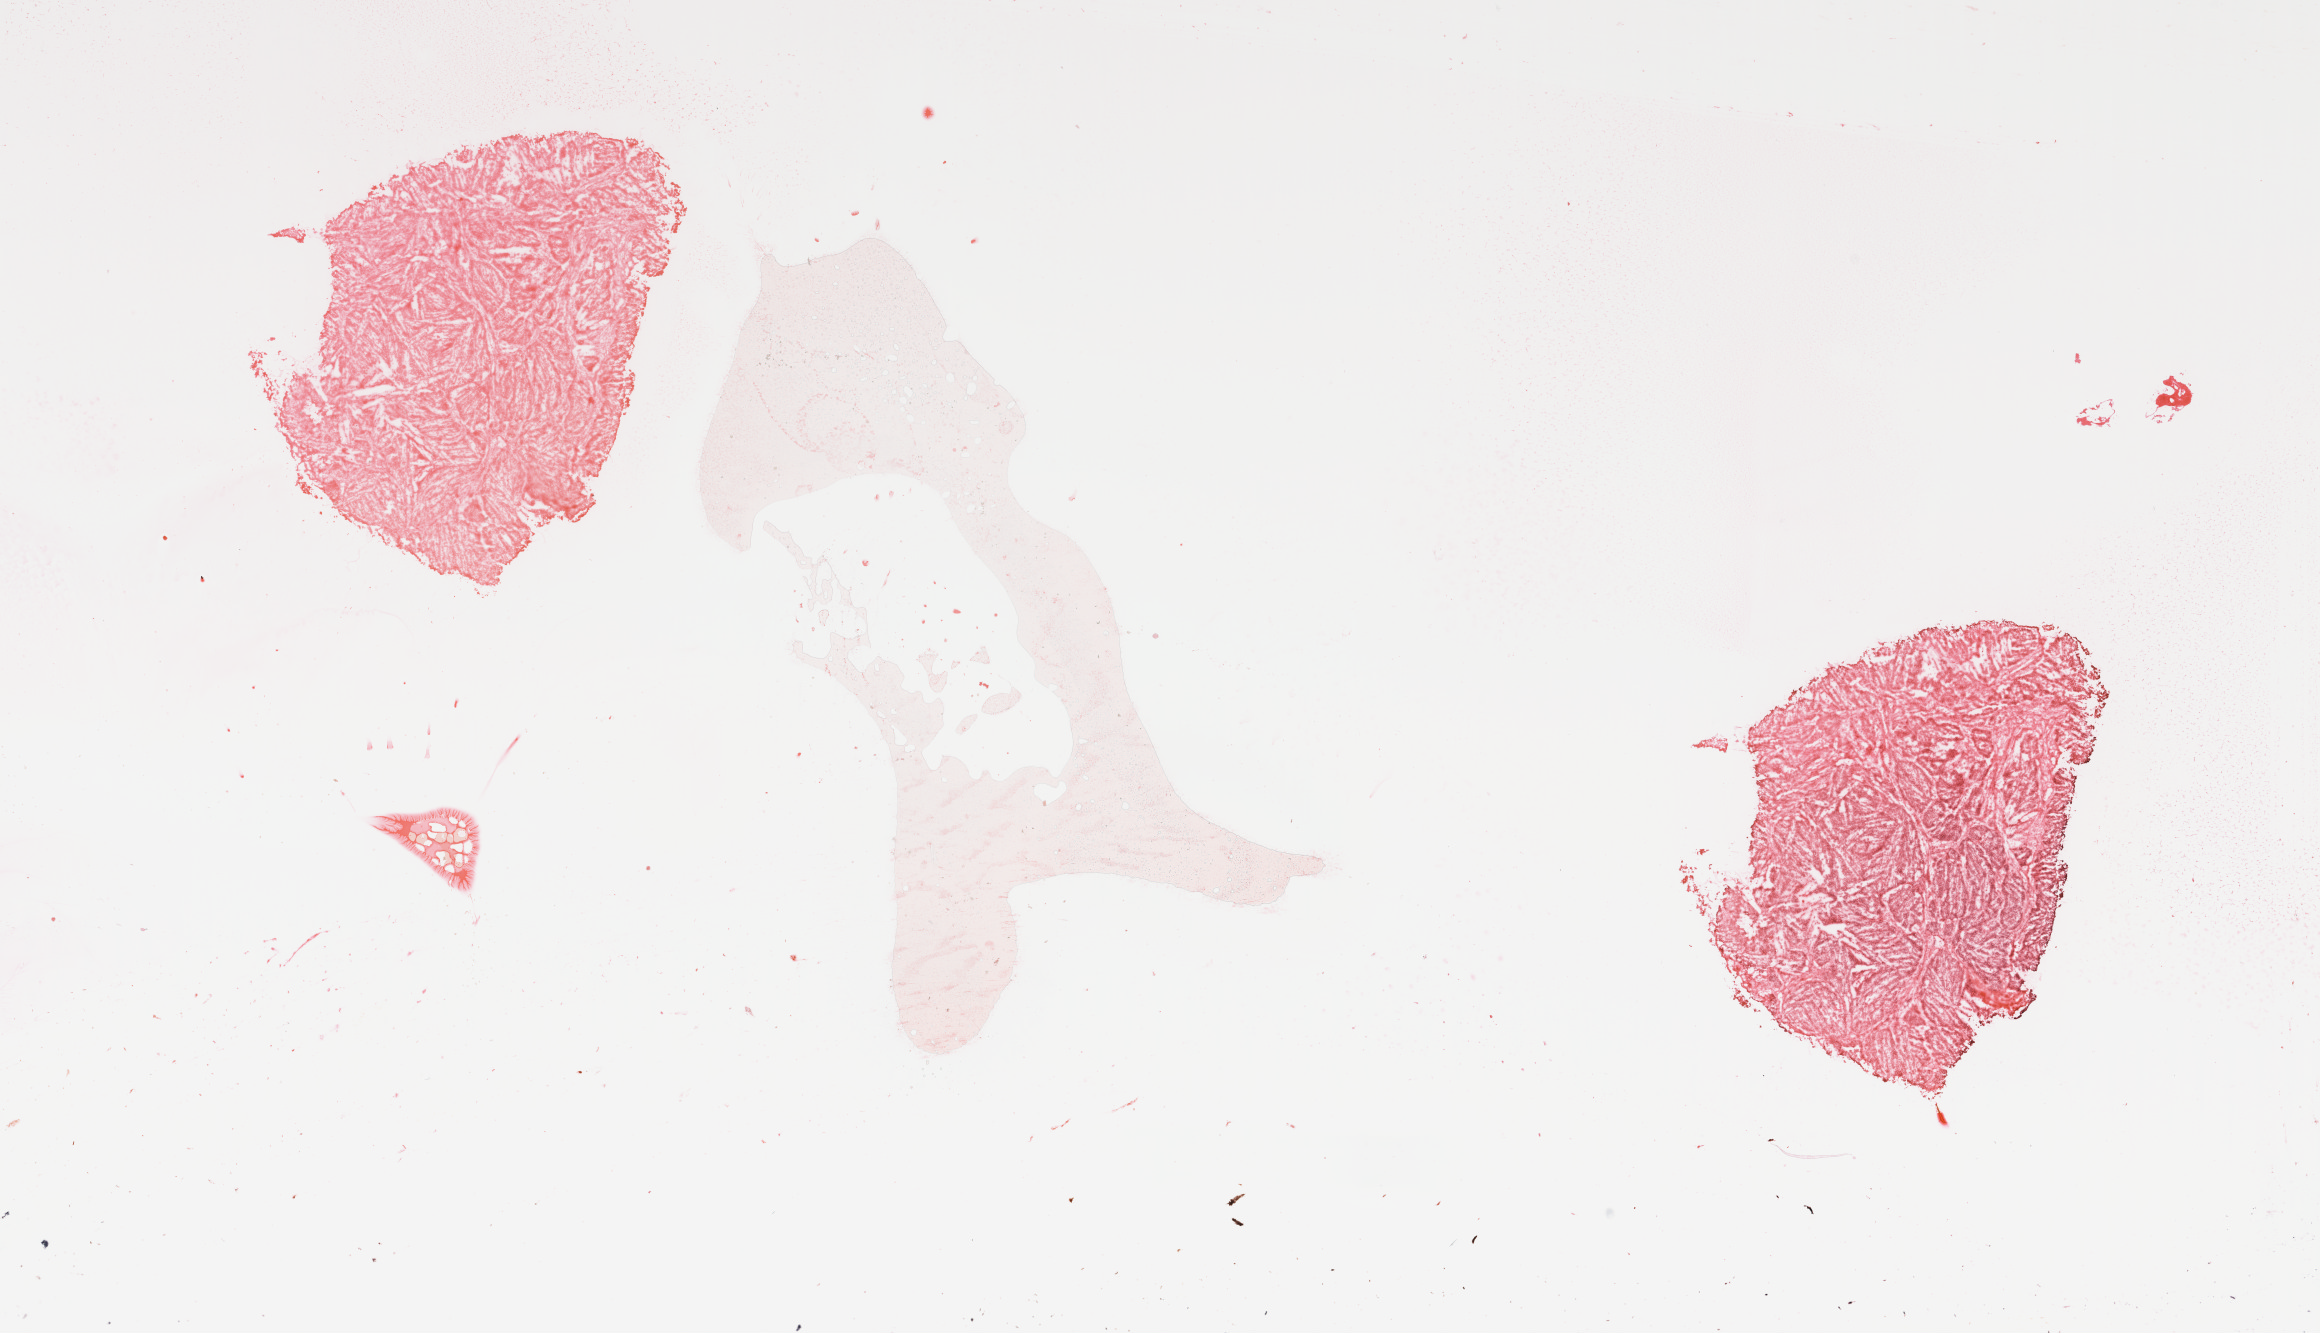
H&E whole-slide image, whole scanned area (about 18.4 x 10.6 mm) shown as a low-resolution overview. Frozen section. Lung, primary tumour sample. Patient: male, age at initial diagnosis 53 years. Slide review estimates, as recorded: tumour cells 100%, tumour nuclei 95%, normal cells 0%, stromal cells 0%, necrosis 0%. Infiltration values recorded for this section: lymphocyte infiltration 0%, monocyte infiltration 0%, neutrophil infiltration 0%.
• diagnosis: Basaloid squamous cell carcinoma (lower lobe, lung)
• AJCC pathologic stage: IA (6th edition)